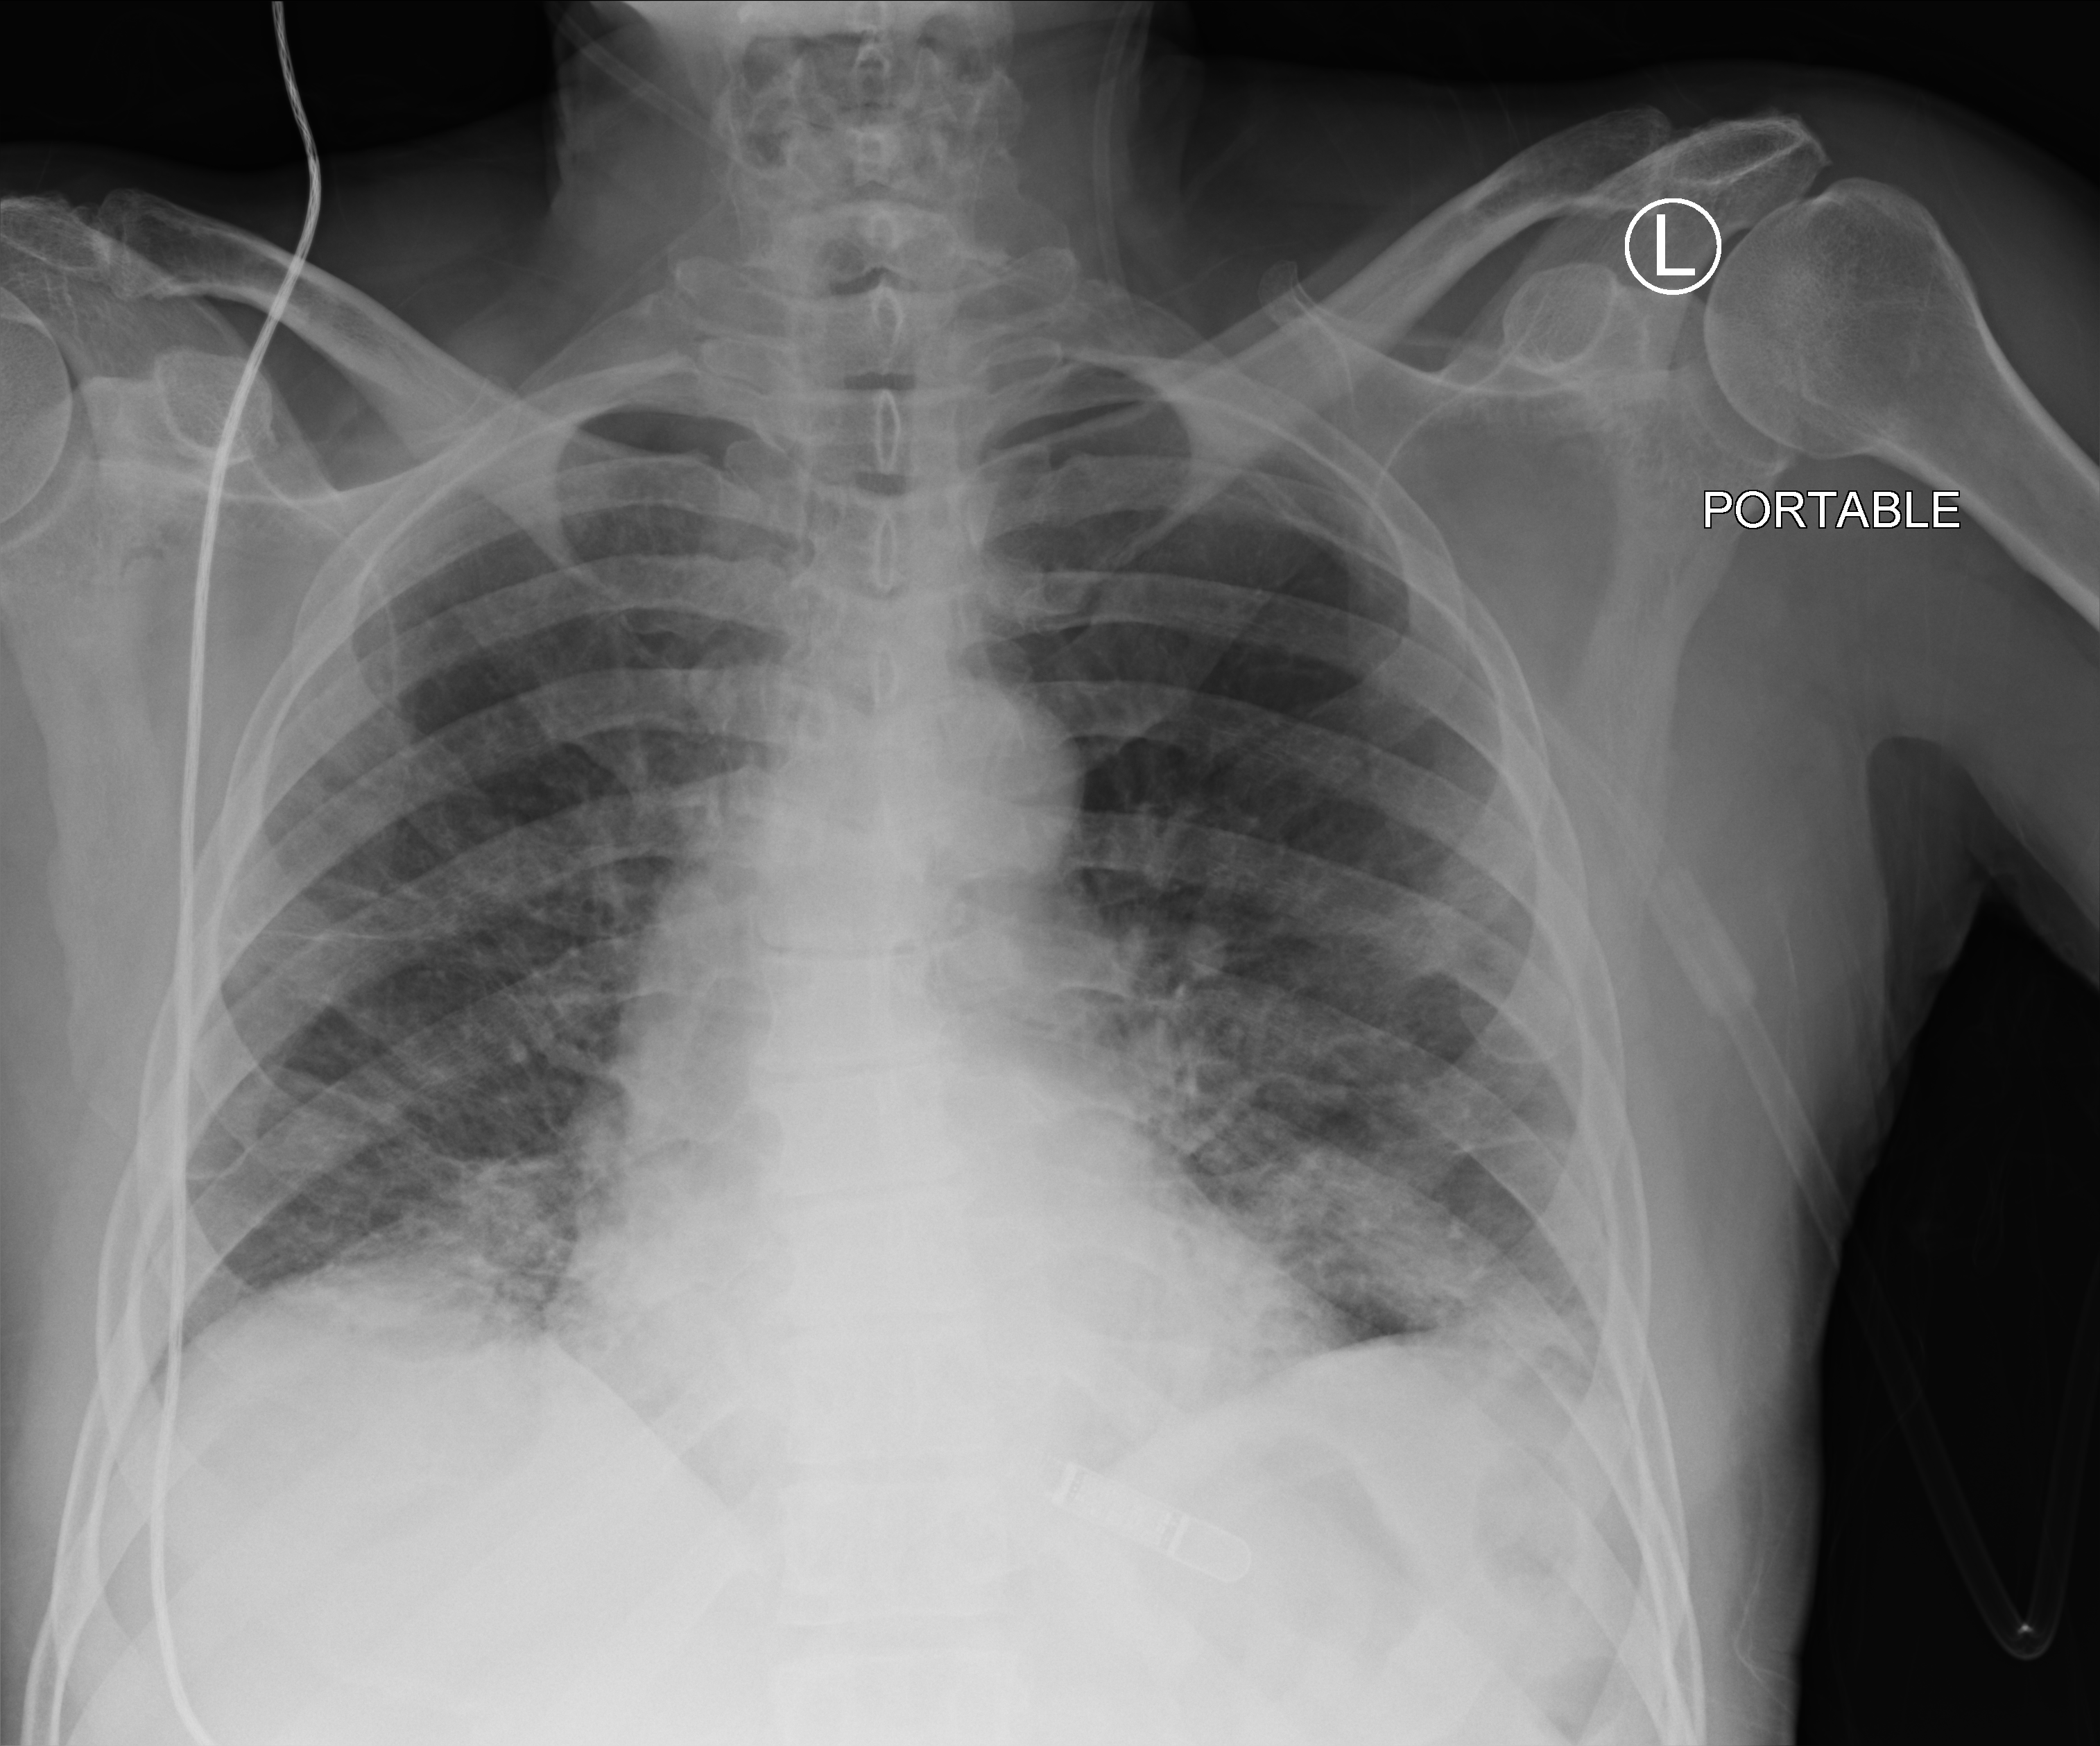
Chest X-ray (portable). Male patient hospitalised with COVID-19, age 75–90 years.
Hospital-stay facts (about this admission, not read from this image; timing relative to this image not recorded): mechanically ventilated during this hospital stay: no.